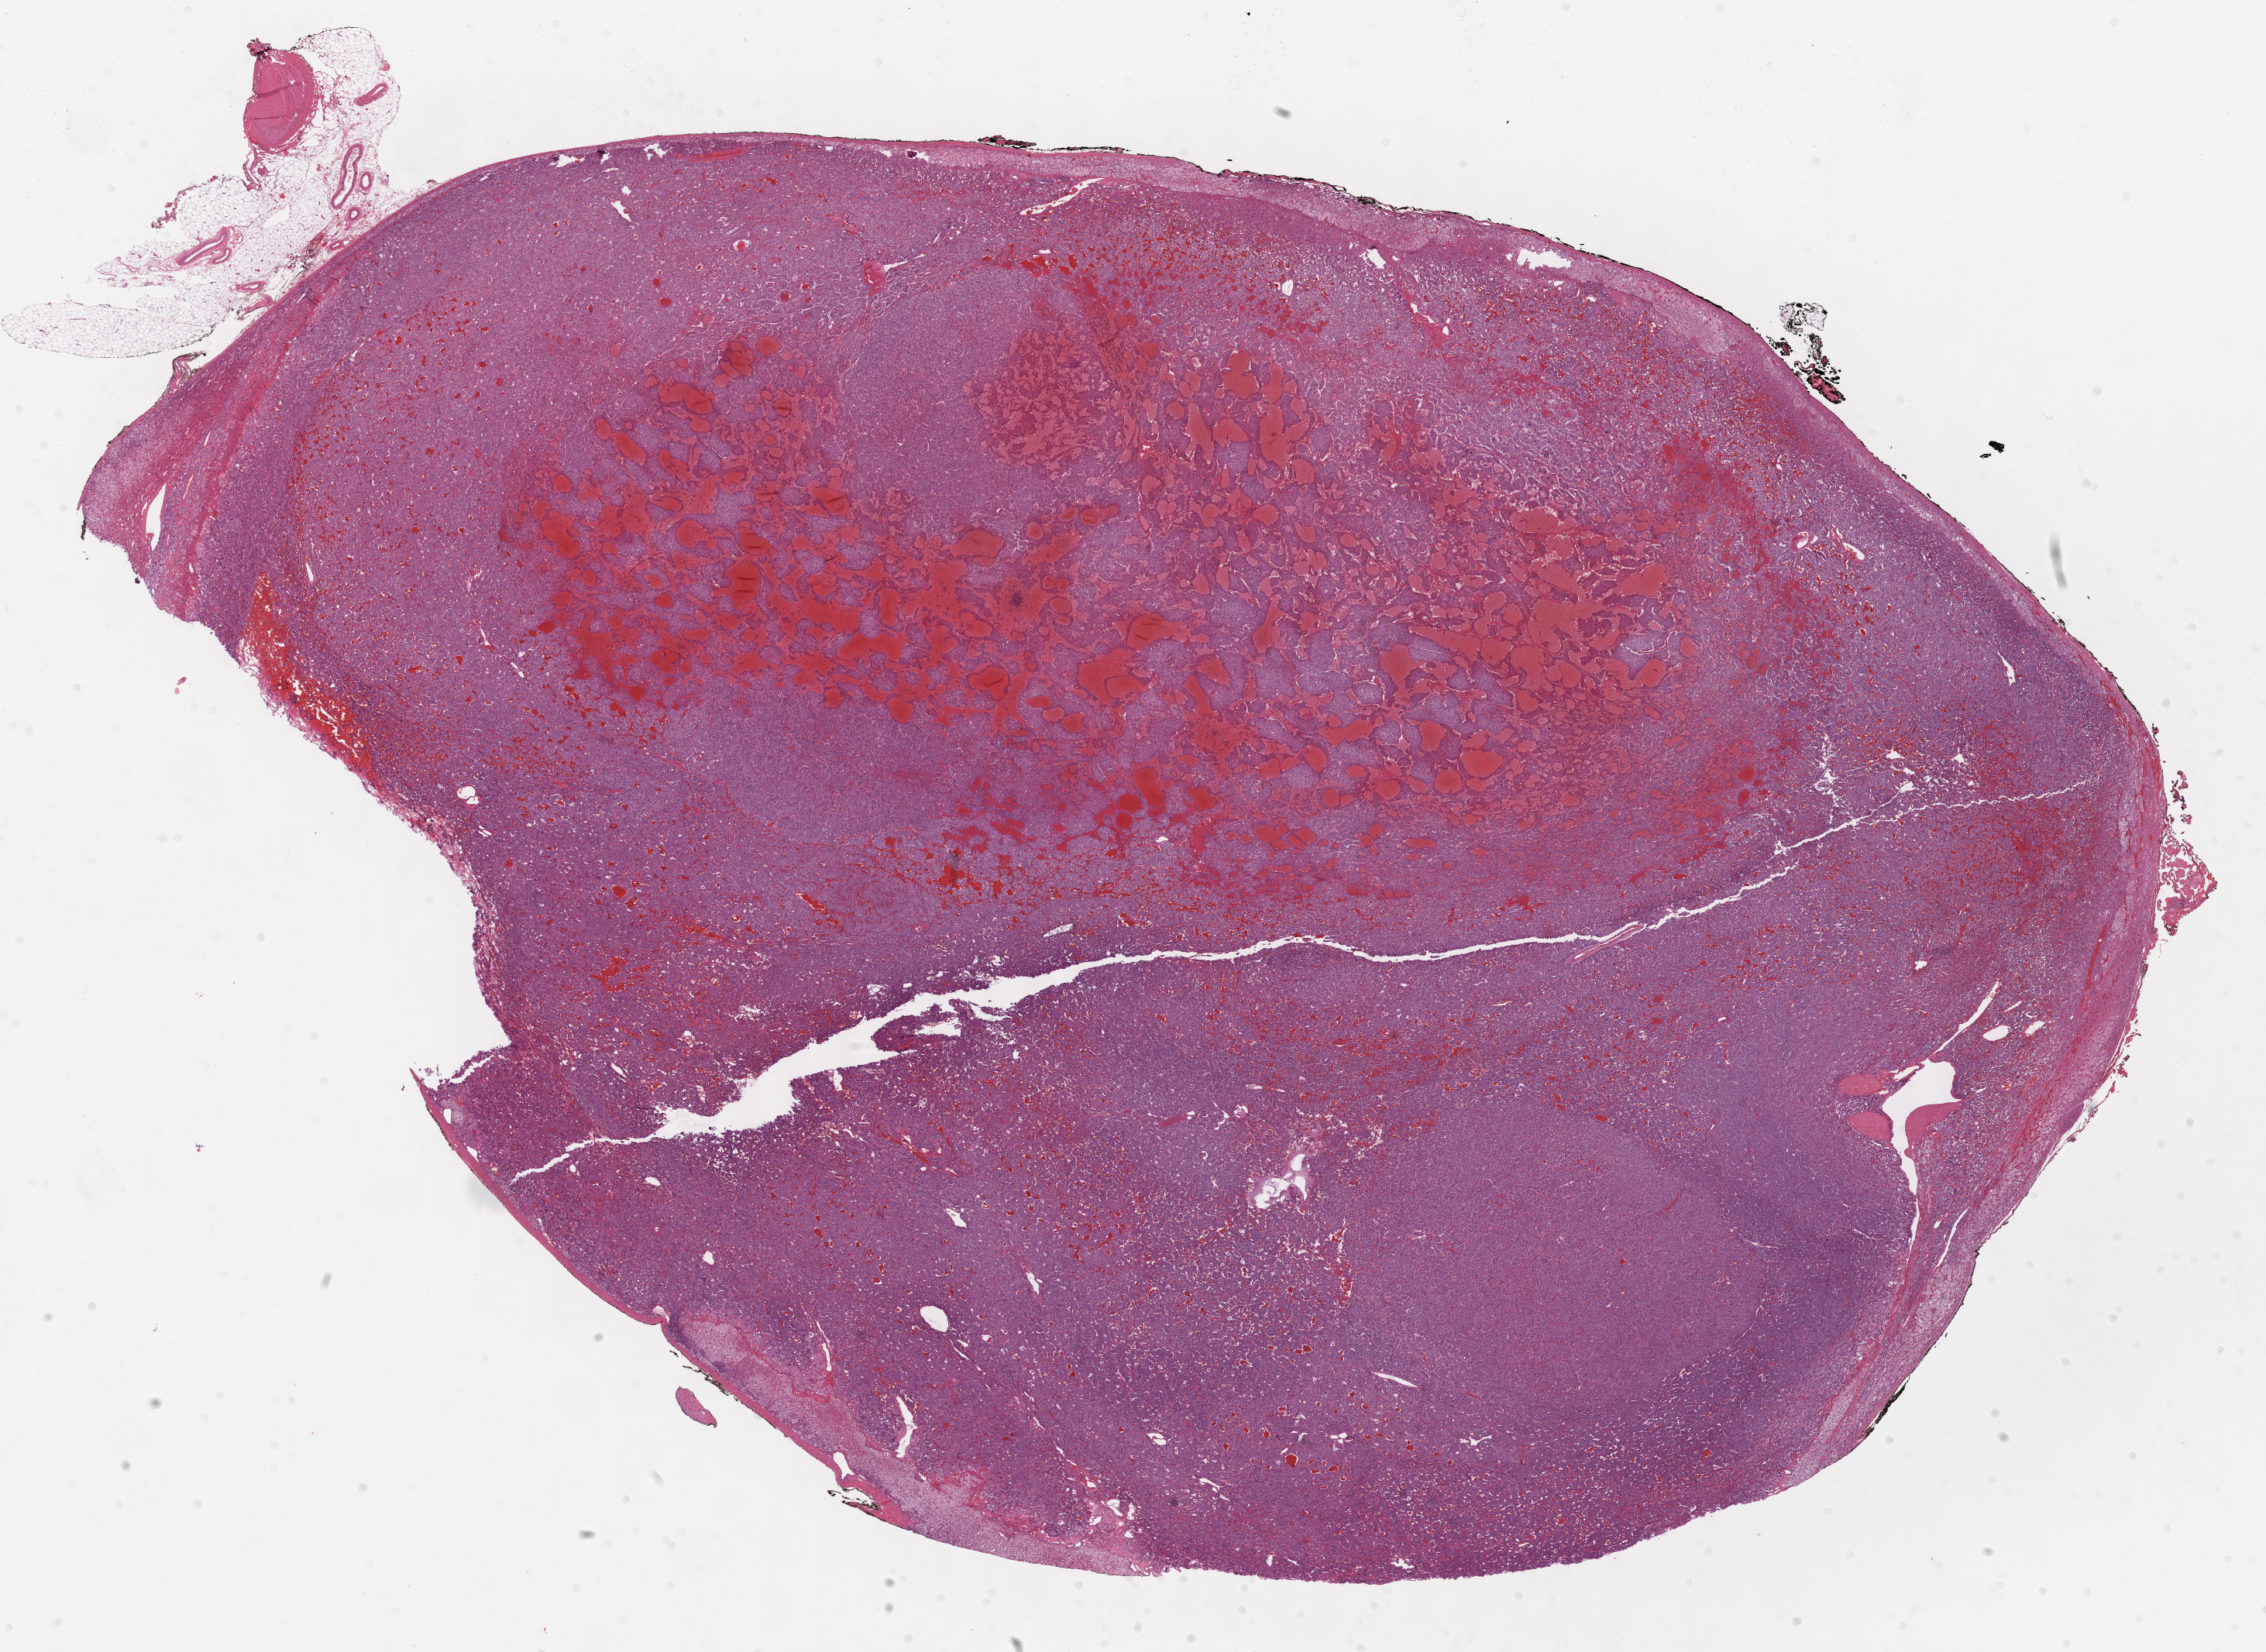
Digitized H&E-stained tissue section (whole slide) — whole scanned area (about 23.7 x 17.3 mm) shown as a low-resolution overview. FFPE section. Primary tumour sample from the adrenal gland. Female, age 25 years at initial diagnosis.
• diagnosis: Pheochromocytoma, NOS